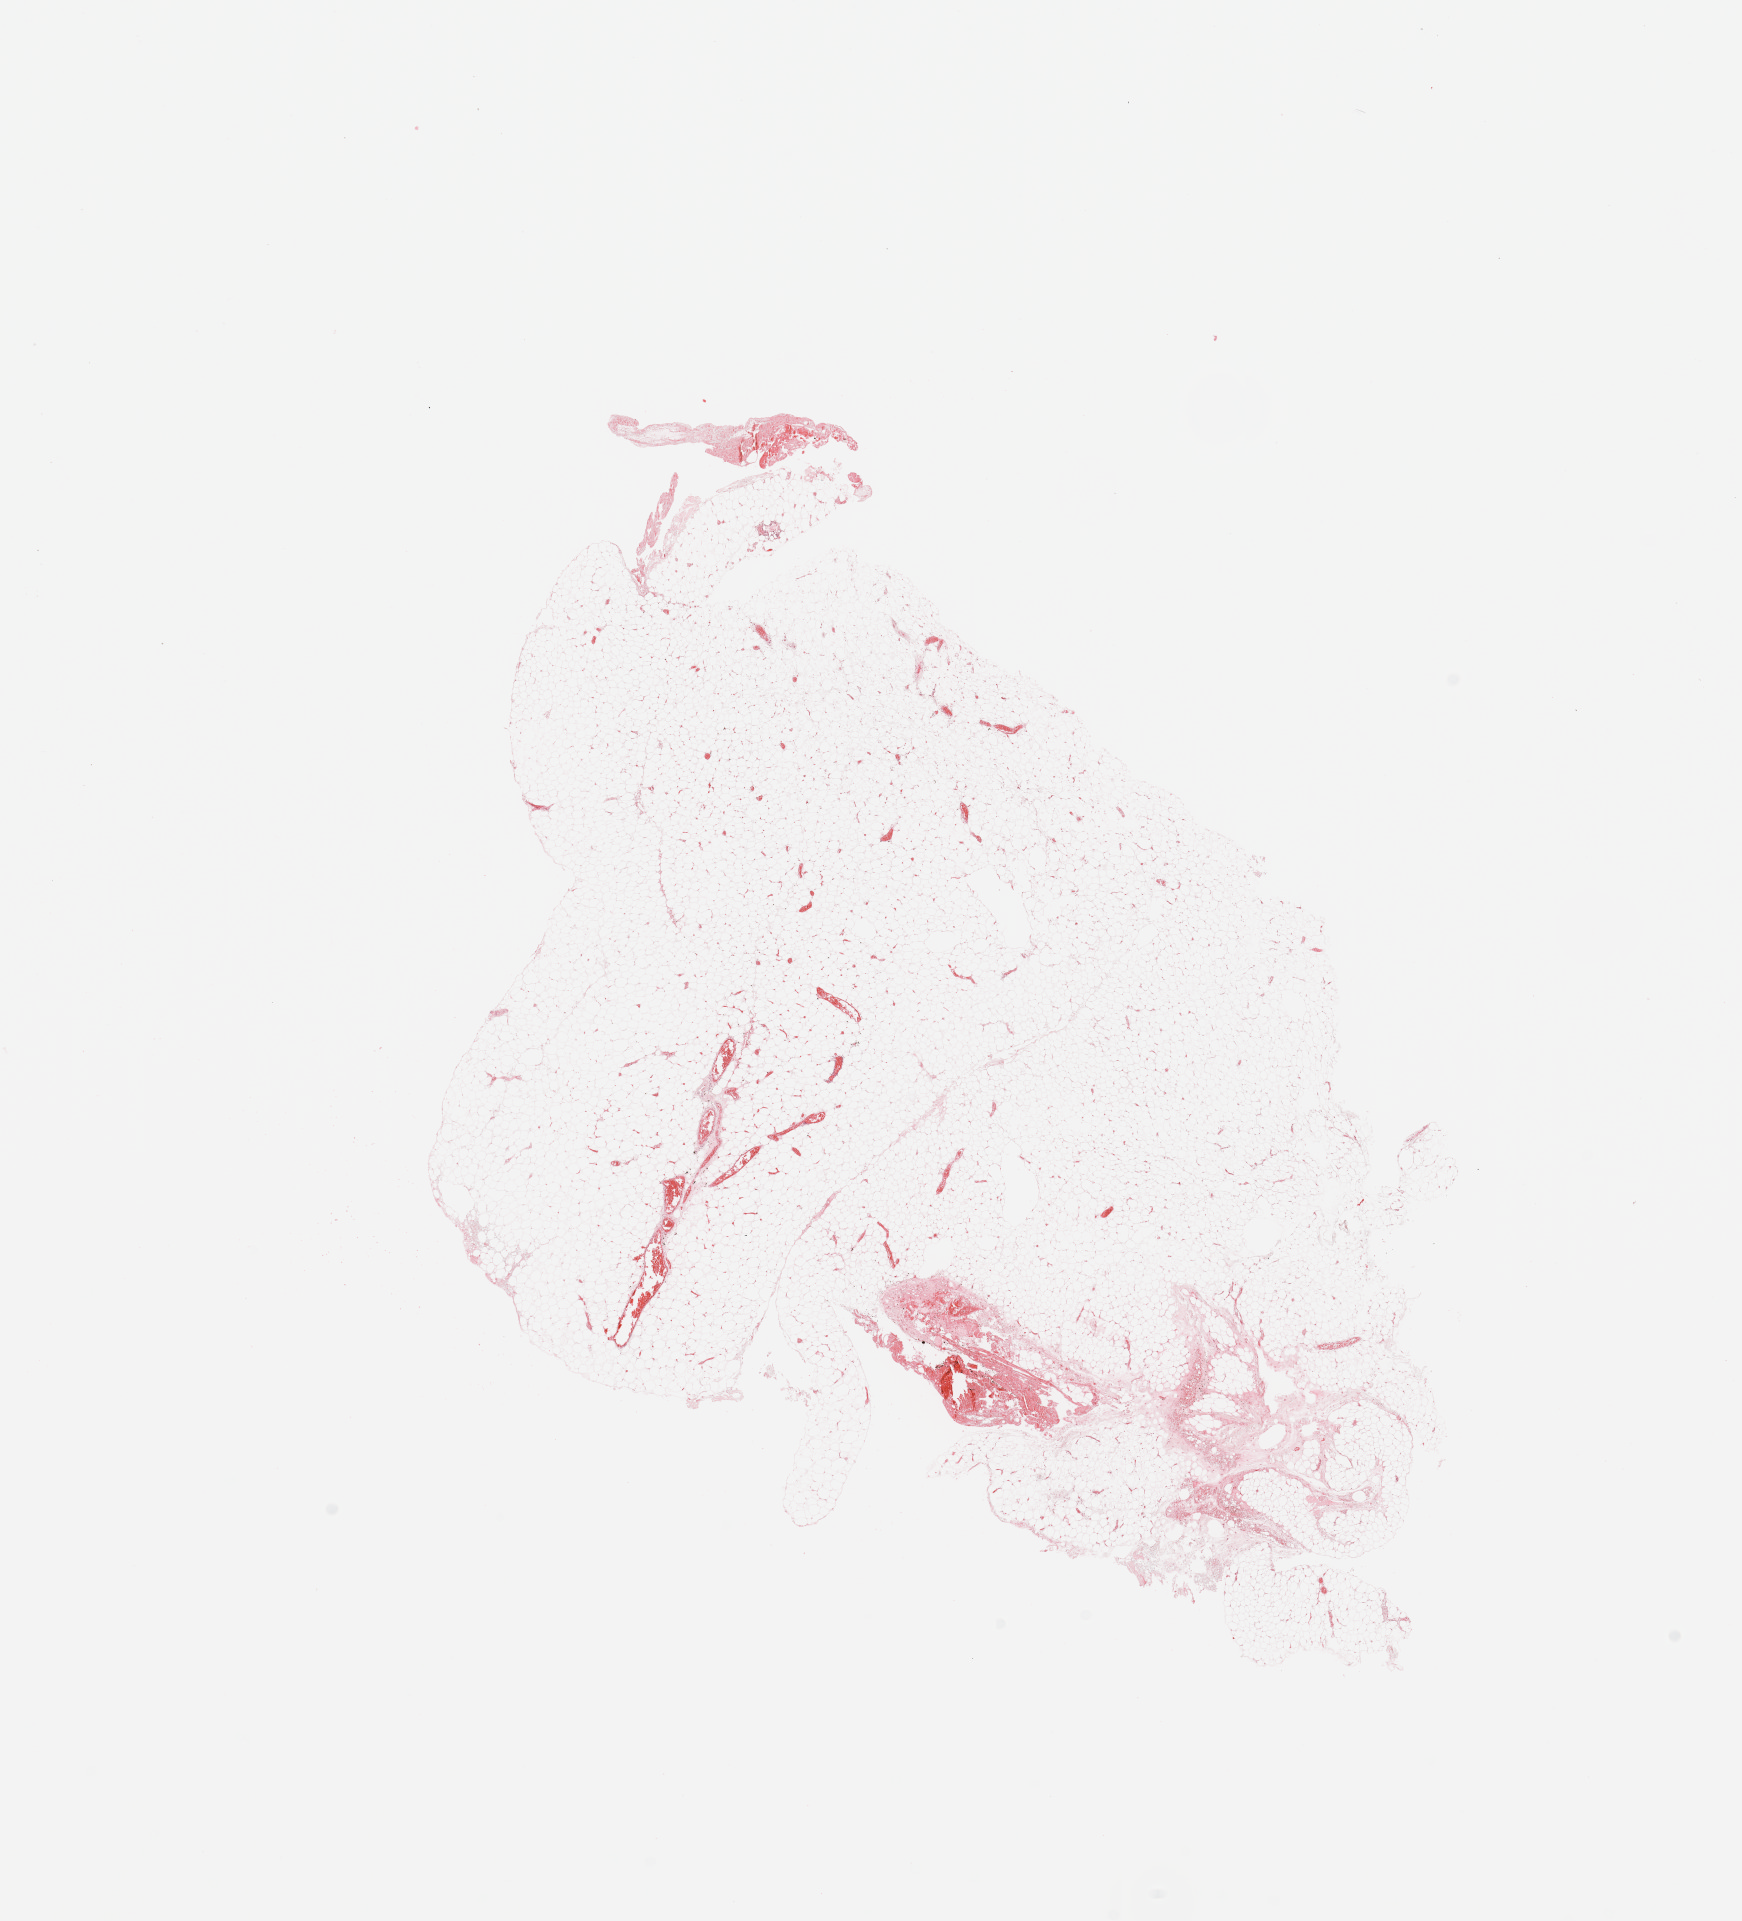
Digitized H&E tissue section (whole slide), low-resolution overview of the scanned area, about 13.8 x 15.2 mm (from a 20x scan), normal (non-tumour) tissue sample. 48-year-old female patient.
- this section: normal (non-tumour) tissue from the same patient
- patient diagnosis (cohort enrolment): sarcoma (site not recorded at cohort level)